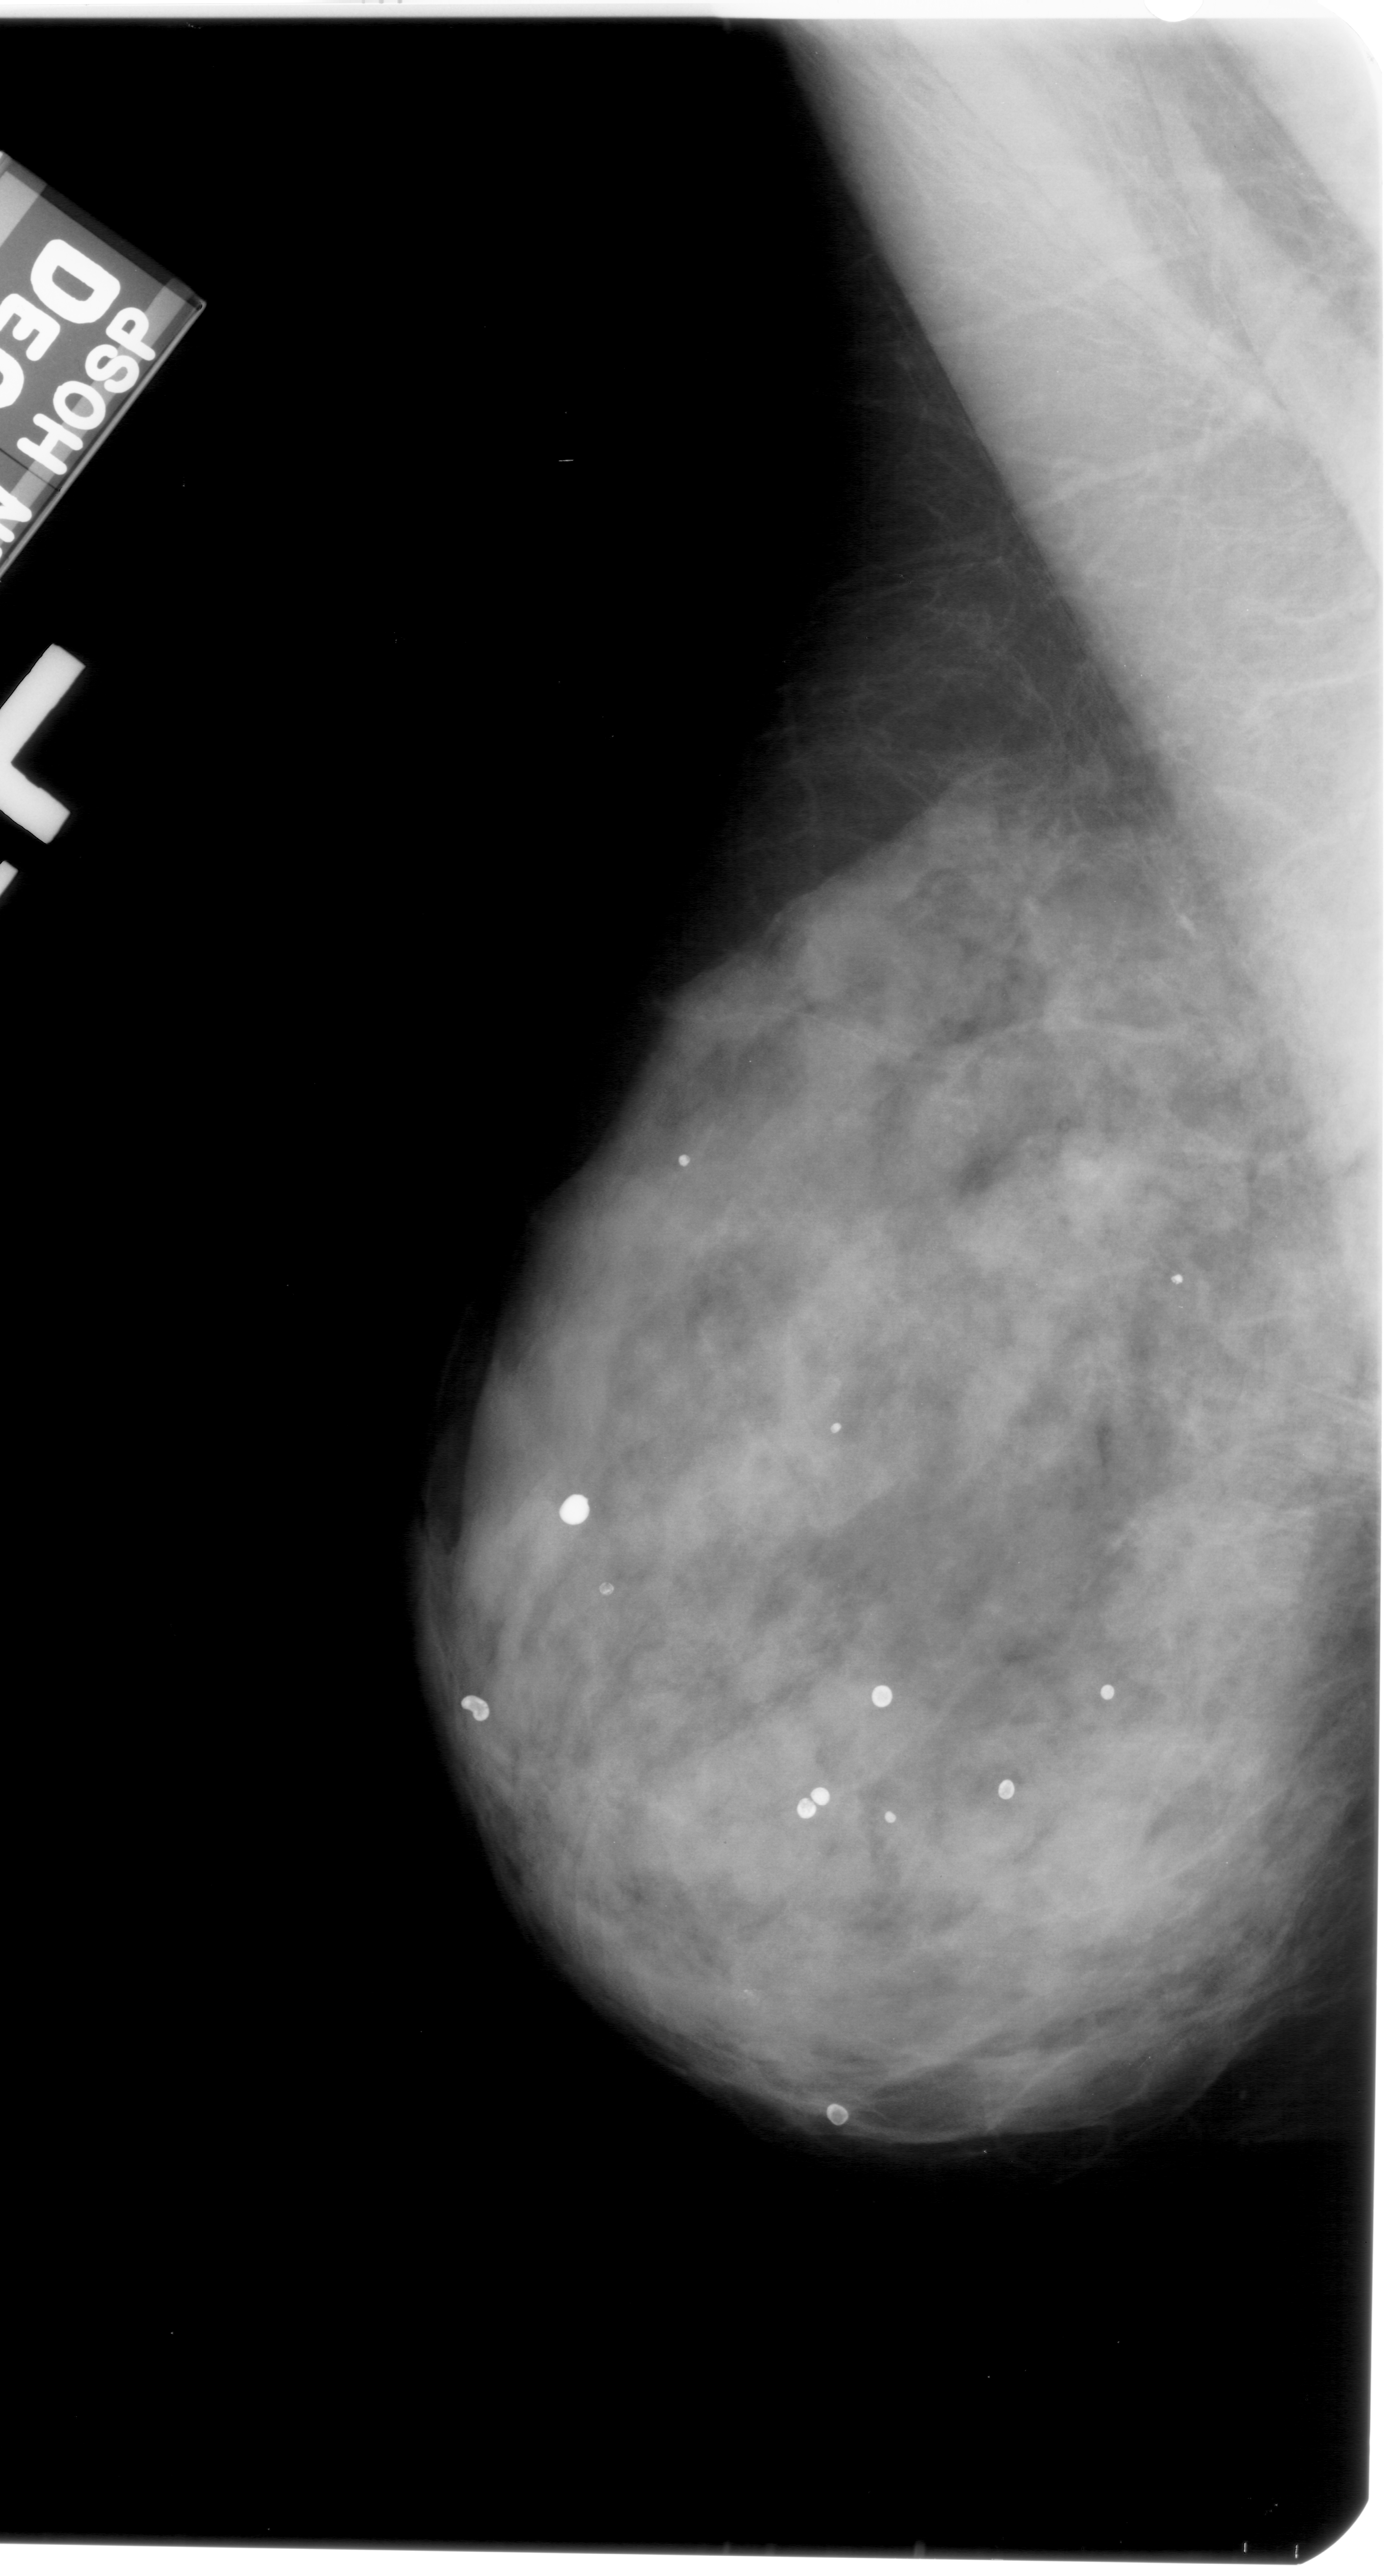
Mammogram (digitized film). Left breast. MLO view. BI-RADS breast density category 4 (scale 1–4). 1387 × 2576 image matrix.
Expert-marked regions of interest on this film, with their recorded descriptors:
- calcifications, morphology amorphous, distribution clustered; BI-RADS assessment category 4; subtlety rating 2 on a 1 (subtle) to 5 (obvious) scale; pathology result (as recorded, not read from the image): benign: bounding box [x1, y1, x2, y2] px = [672, 1918, 829, 2071]